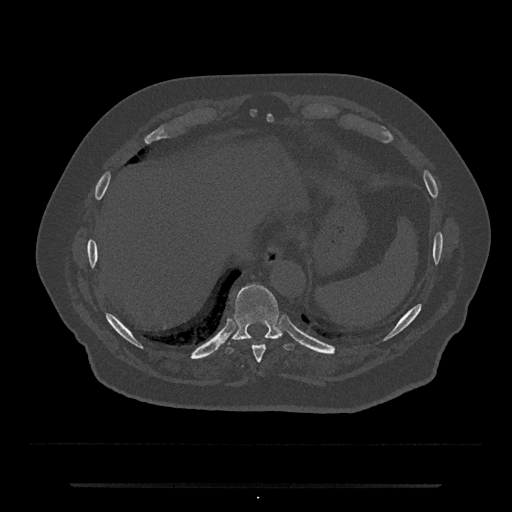
CT including the spine, one axial slice; reconstruction kernel Br40s/3; bone window (W 1800 / L 400 HU); 512 × 512 image matrix, field of view 434 × 434 mm. Patient: male, 80 years. Case-level facts recorded for this patient, not image findings: primary cancer: prostate; vertebrae with lytic lesions (as recorded): L1, T11.
Outlined on this slice (semi-automatic segmentation, software-assisted and operator-edited):
- T10 vertebra: bounding box [x1, y1, x2, y2] px = [226, 284, 295, 354]
- T9 vertebra: [252, 345, 265, 363]